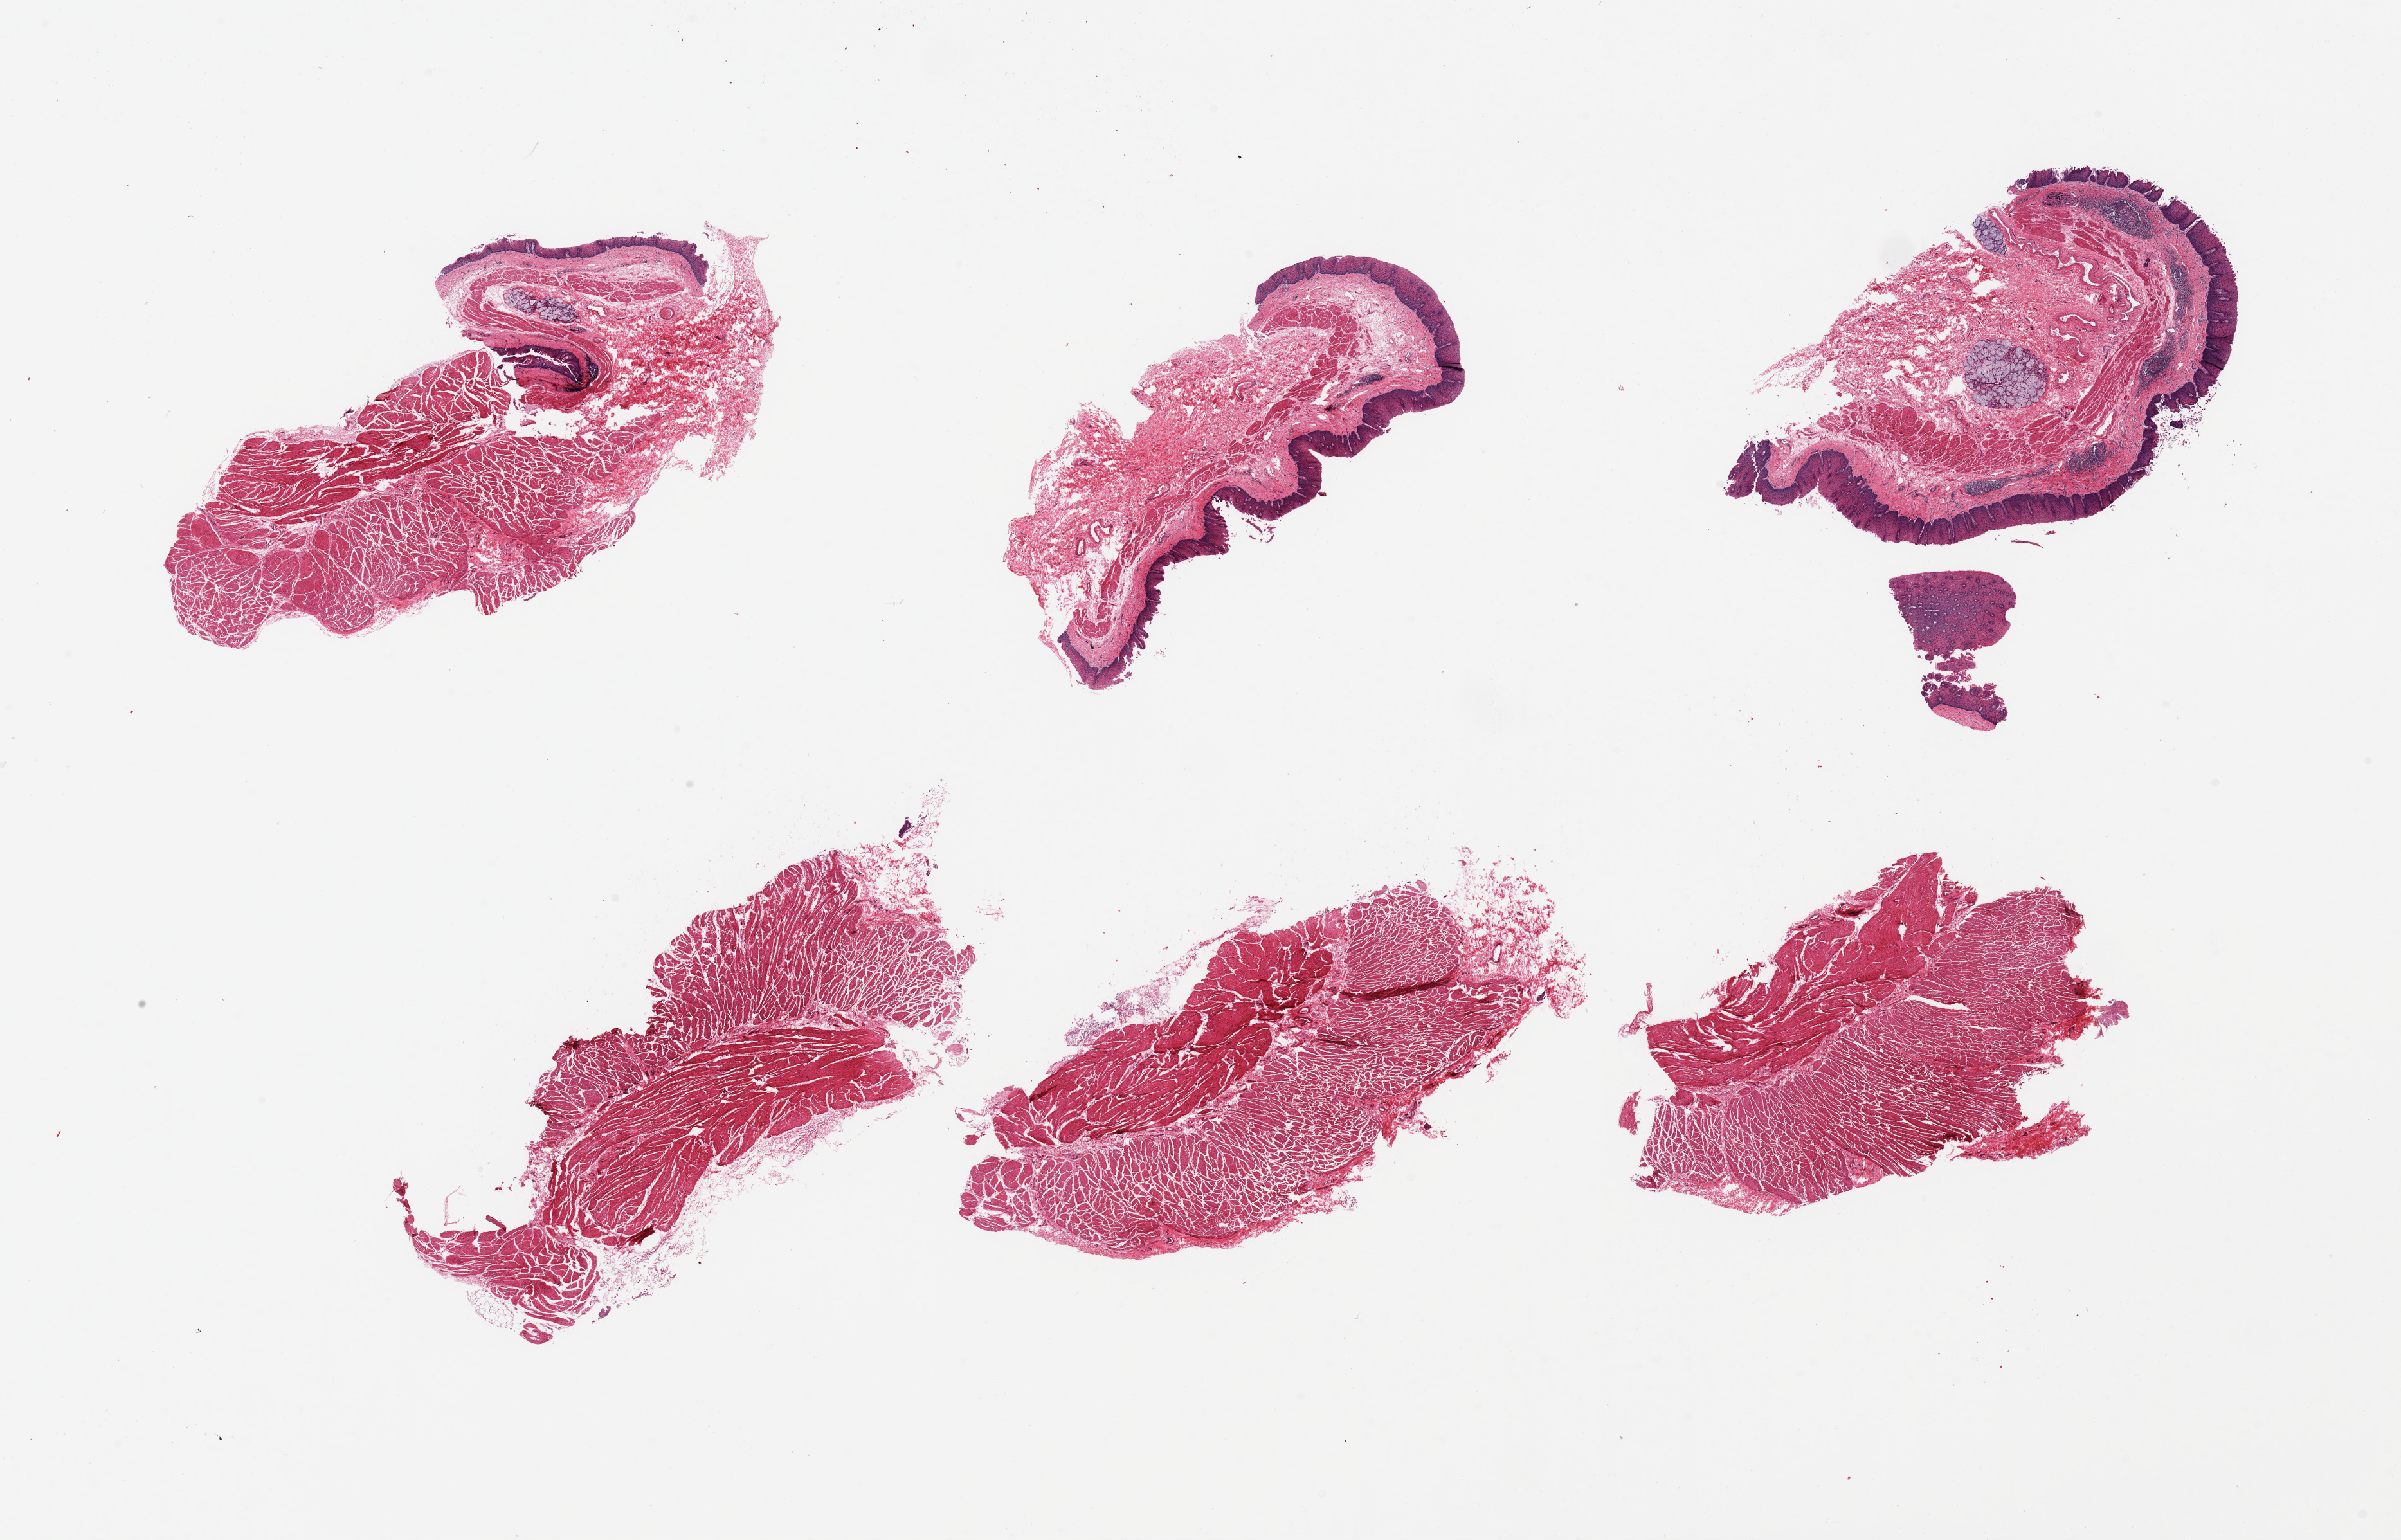
Digitized H&E-stained section, brightfield — whole scanned area (about 29.5 x 18.9 mm) shown as a low-resolution overview.
- specimen: PAXgene-fixed paraffin-embedded (PFPE) section; sampled site (target tissue): gastroesophageal junction; donor tissue sample